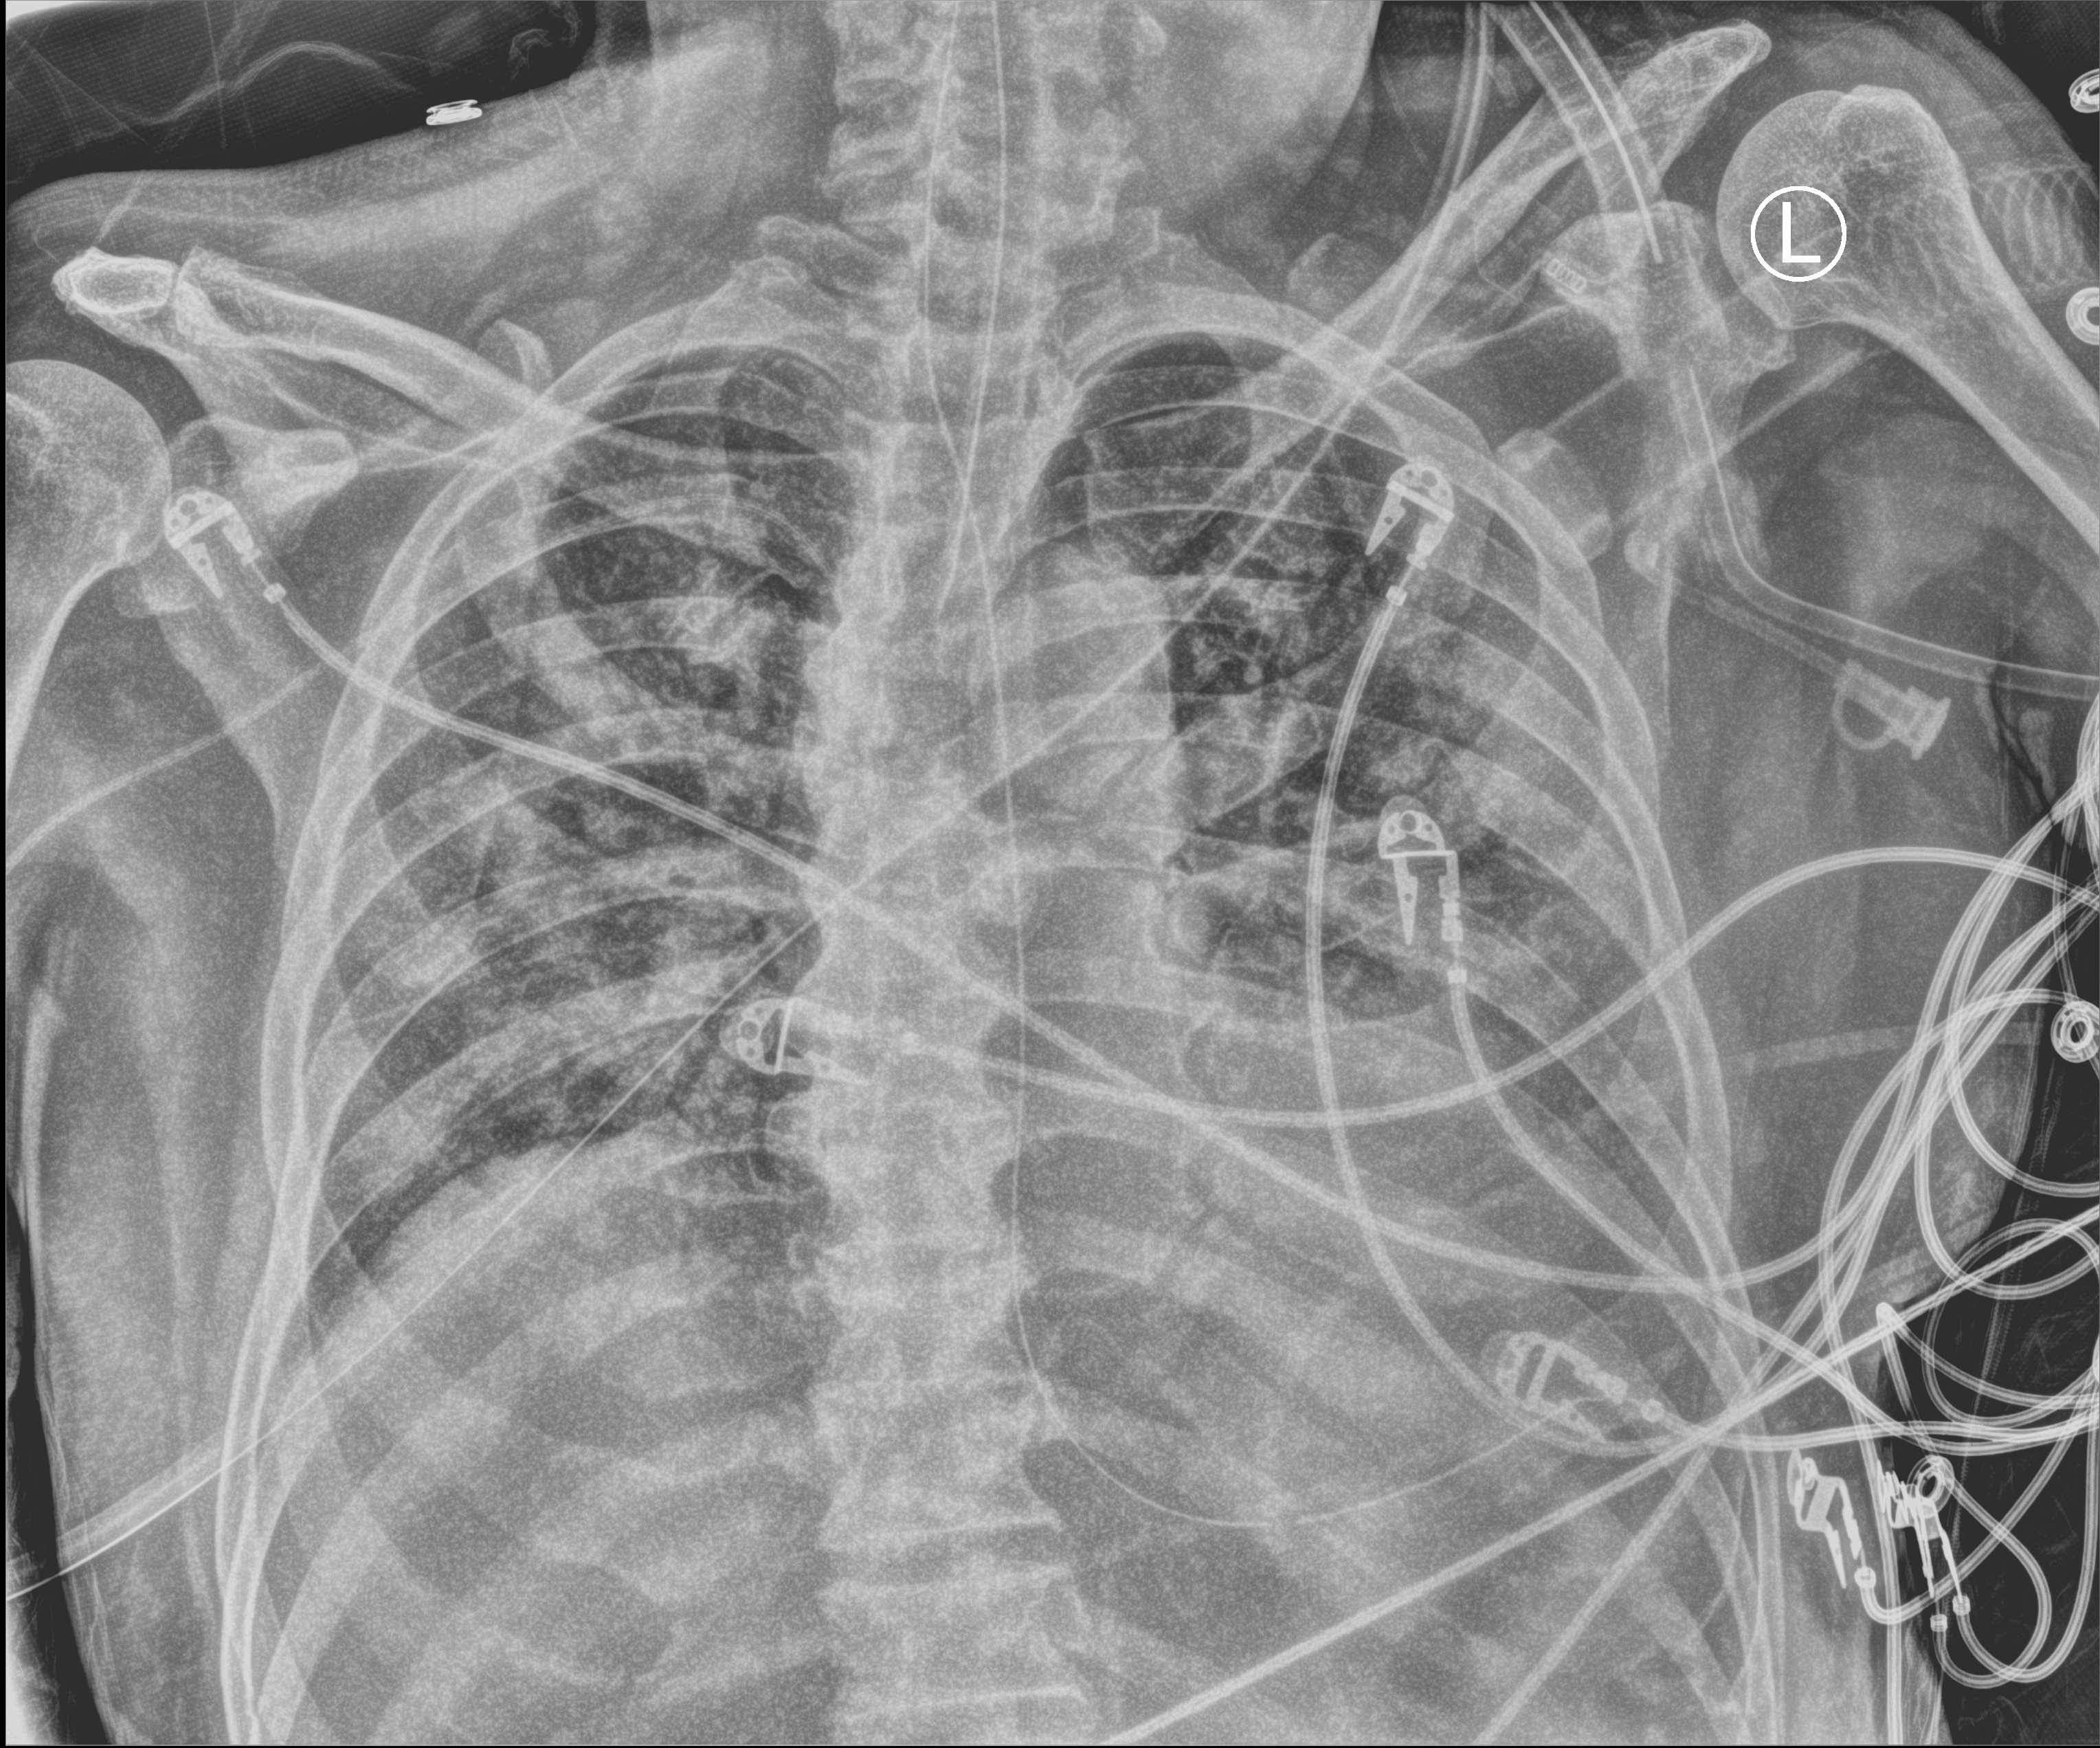
Bedside chest radiograph (computed radiography), anteroposterior (AP) projection. Male patient hospitalised with COVID-19, age 75–90 years.
Hospital-stay facts (about this admission, not read from this image; timing relative to this image not recorded):
- length of hospital stay: 33 days